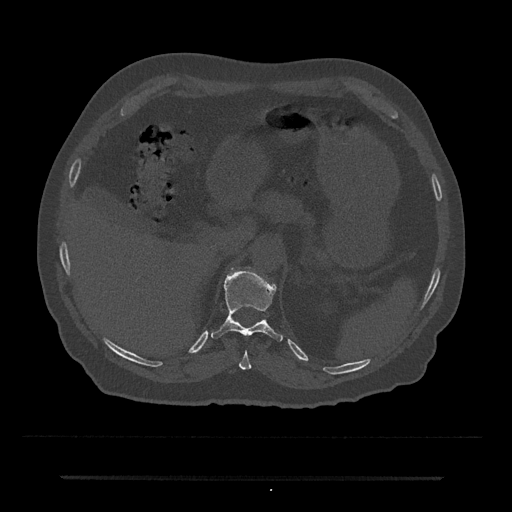
CT including the spine, one axial slice. Position 182 of 797 along the scan axis. Reconstruction kernel Br40s/3. Bone window (W 1800 / L 400 HU). 0.5 mm slice thickness. 512 × 512 image matrix, field of view 437 × 437 mm. Male patient, age 69 years. Case-level facts recorded for this patient, not image findings: primary cancer: prostate.
Structures marked on this image (semi-automatic segmentation, software-assisted and operator-edited):
- T10 vertebra: box from (x=239, y=351) to (x=252, y=370) px
- T11 vertebra: (x=211, y=270)–(x=283, y=342)